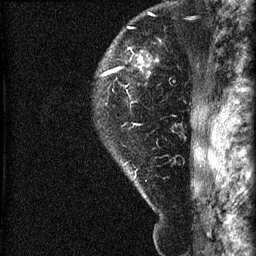
Breast MRI (dynamic contrast-enhanced), one sagittal slice; slice 54 of 60 in the series (ordered by position); dynamic contrast-enhanced series, image 2 of 3 at this slice position (ordered by acquisition); 1.5 T; TE 4.2 ms, TR 22.7 ms; 256 × 256 image matrix, field of view 180 × 180 mm. Patient: female, 45 years. Case-level facts recorded for this patient, not image findings: setting: breast cancer imaged before/during neoadjuvant chemotherapy; receptor status: HR-positive, HER2-negative.
Annotated regions visible in this slice (semi-automatic segmentation, software-assisted and operator-edited):
- analysis volume of interest (the breast-tissue region the enhancement analysis was run in; not a lesion): bounding box <93,11,205,140> (left, top, right, bottom; pixels)
- tumour enhancement mask (voxels above the 90 % enhancement threshold inside the analysis volume of interest): <103,68,119,75>